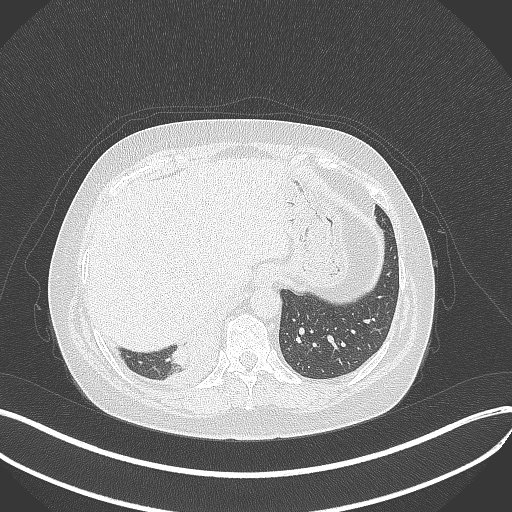
Chest CT, one axial slice. Position 75 of 381 along the scan axis. 120 kVp. Lung window (W 1500 / L -600 HU). 512 × 512 image matrix. Patient: female, 56 years. From the clinical record (not read from this slice): clinical TNM (as recorded): T2b N1 M0; histopathological grade: G3.
Structures marked on this image (rectangle marked by the reading radiologist):
- lung tumour (recorded histology: small cell carcinoma): bounding box [x1, y1, x2, y2] px = [168, 329, 207, 371]